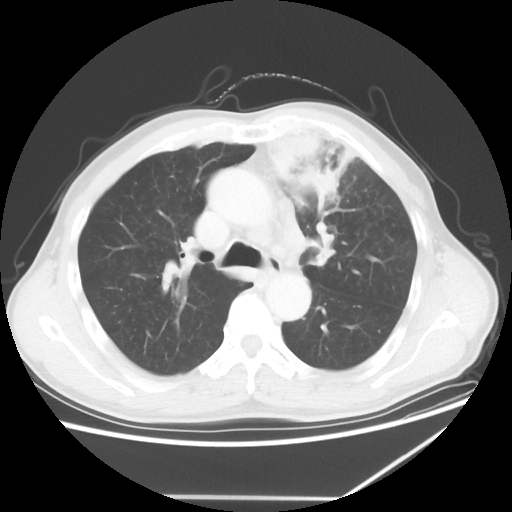
Chest CT, one axial slice. Position 42 of 64 along the scan axis. Lung window (W 1500 / L -600 HU). 512 × 512 image matrix, field of view 383 × 383 mm. Male patient, age 64 years. From the clinical record (not read from this slice): clinical TNM (as recorded): T1c N1 M1; histopathological grade: G2.
Annotated regions visible in this slice (rectangle marked by the reading radiologist):
- lung tumour (recorded histology: squamous cell carcinoma): box from (x=268, y=120) to (x=393, y=286) px